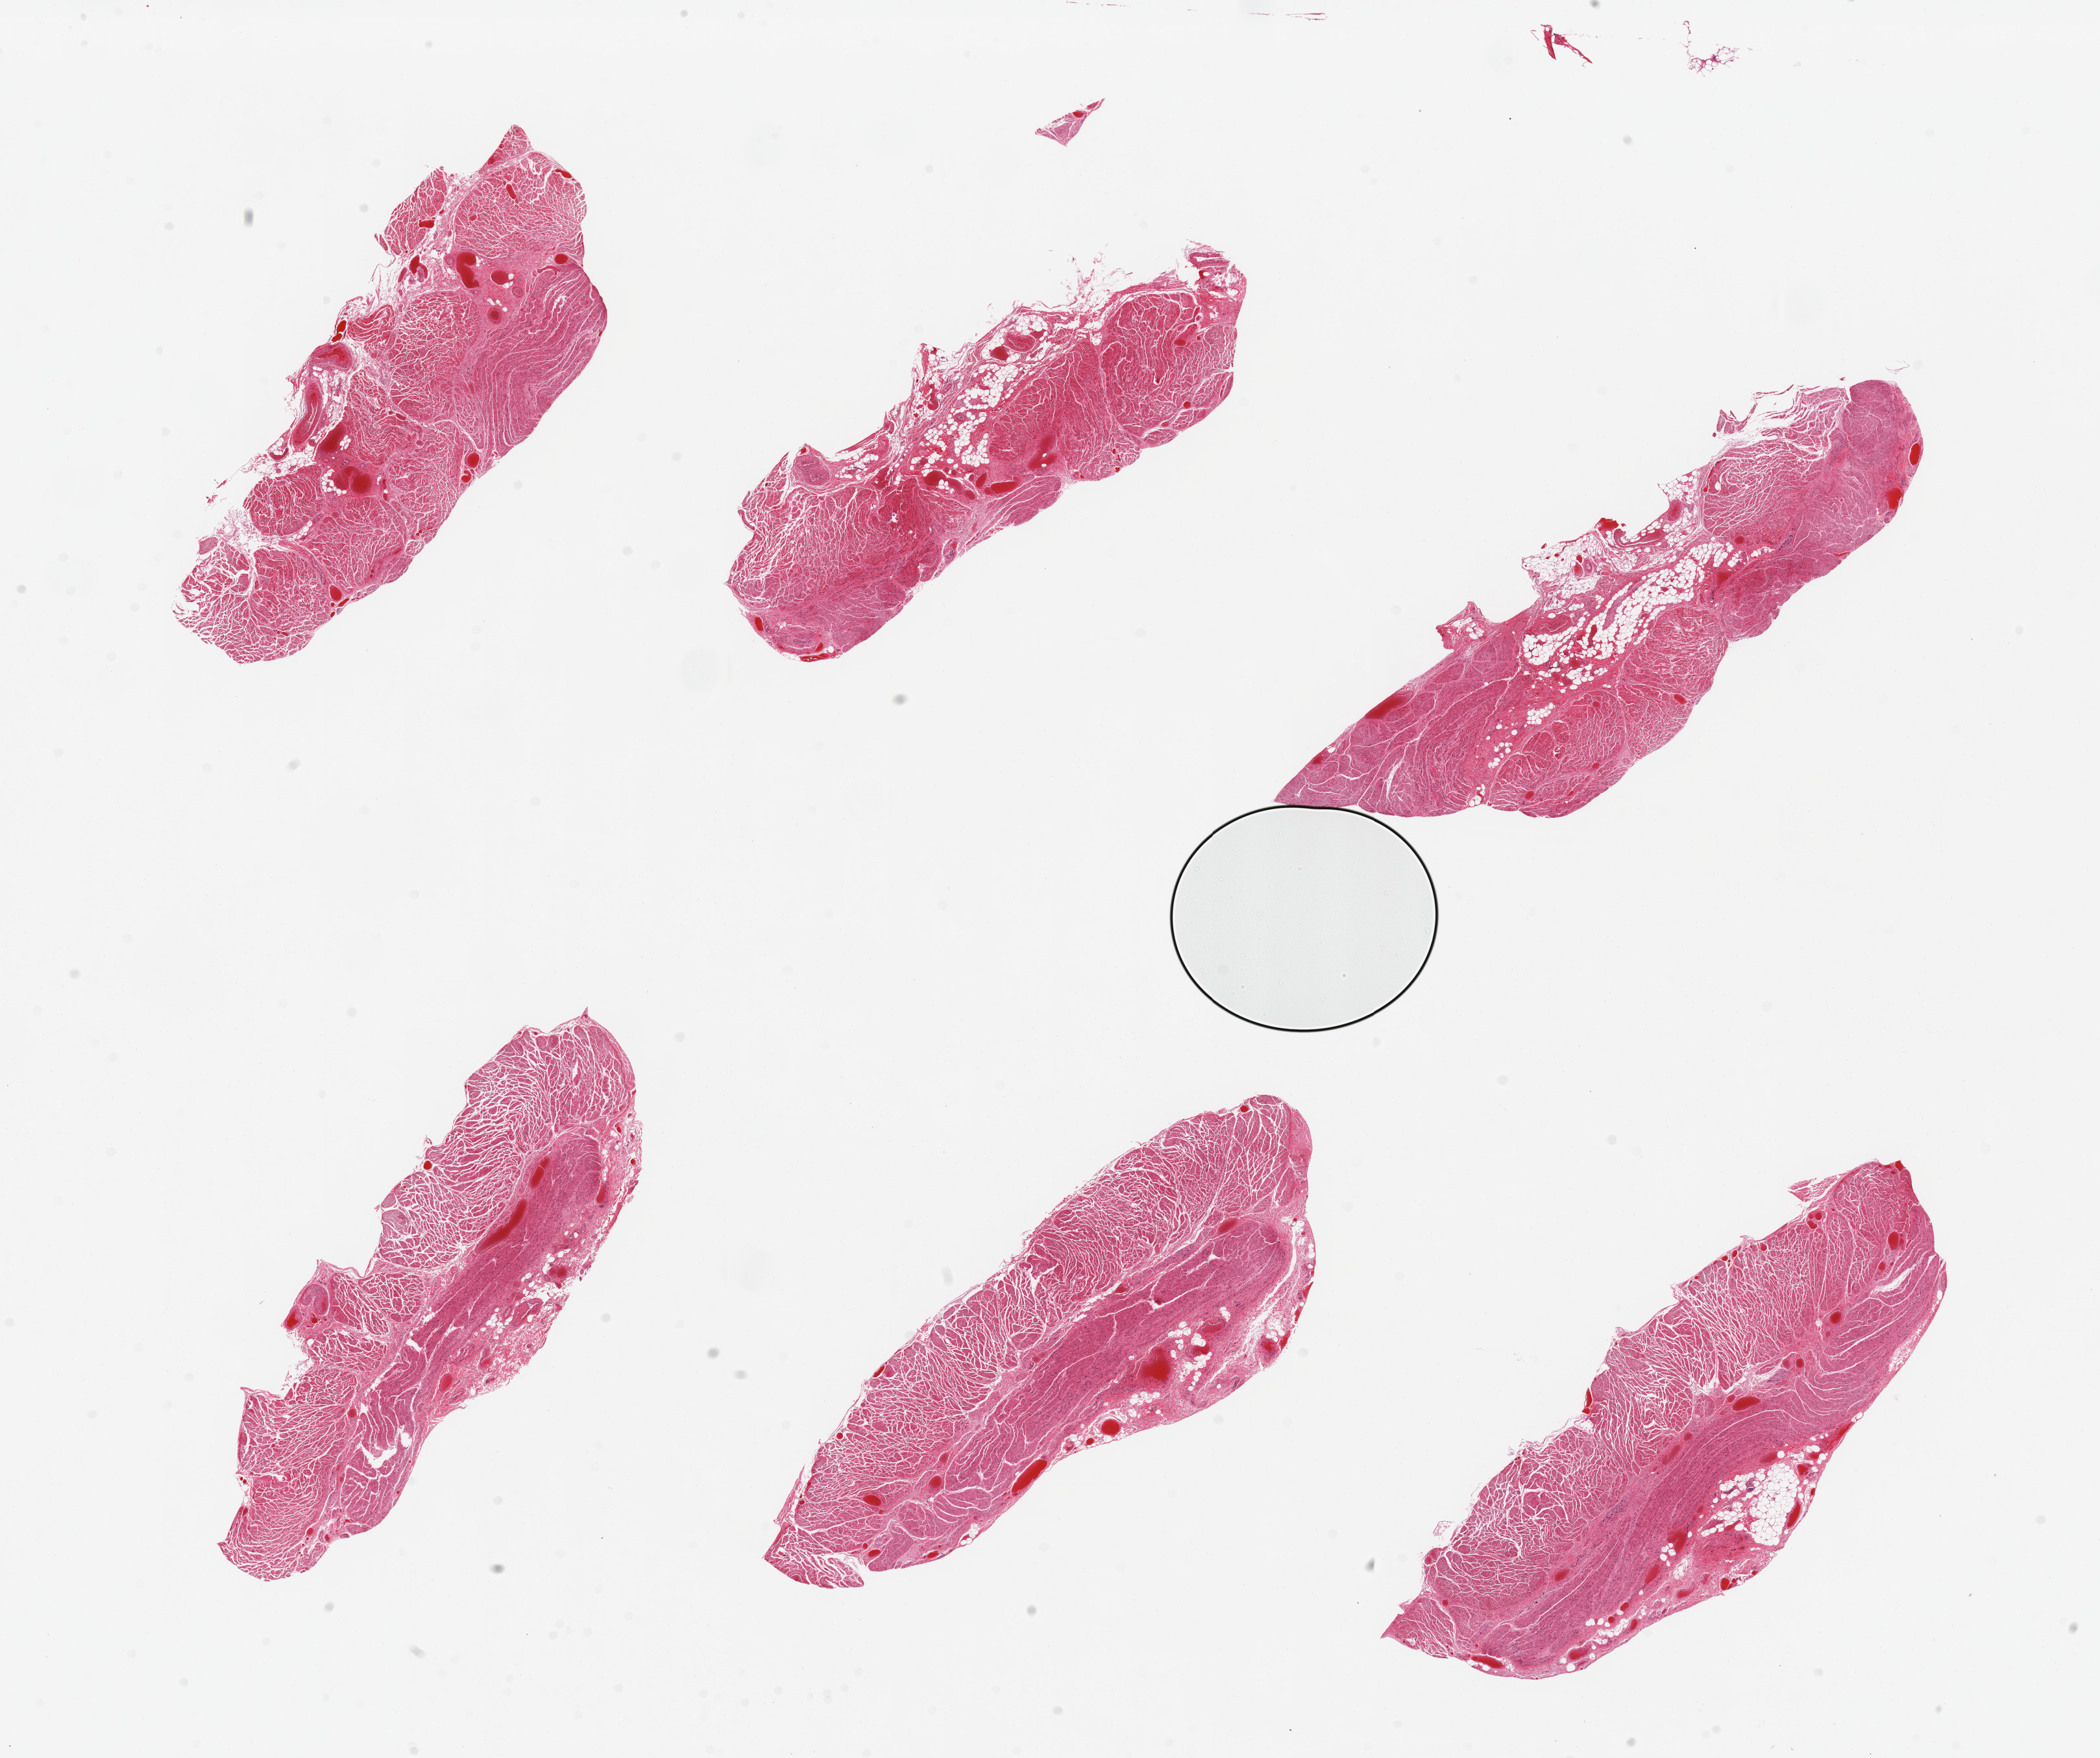
Digitized hematoxylin and eosin (H&E)-stained section, brightfield, low-resolution overview of the scanned area, about 25.6 x 21.4 mm. PAXgene-fixed paraffin-embedded (PFPE) section. Target tissue: gastroesophageal junction. Donor tissue sample.
Reviewer comment on this tissue sample: 6 pieces; up to 10% fat.